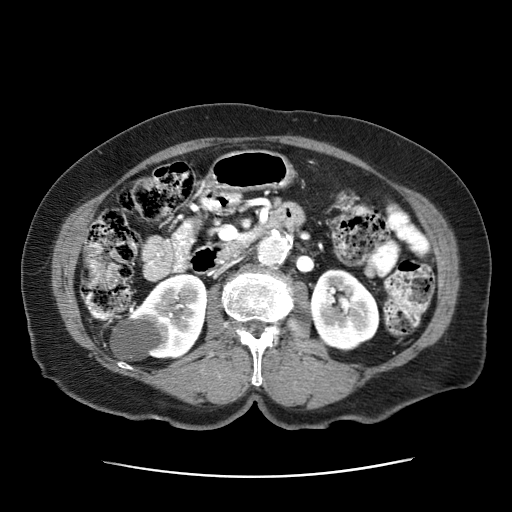
Contrast-enhanced abdominal CT (liver protocol), one axial slice. Position 5 of 63 along the scan axis. Reconstruction kernel STANDARD. 120 kVp. Intravenous contrast given. Soft-tissue window (W 400 / L 40 HU). 2.5 mm slice thickness. 512 × 512 image matrix, field of view 360 × 360 mm. Female patient, age 79 years. From the clinical record (not read from this slice): diagnosis: hepatocellular carcinoma (patient treated with transarterial chemoembolisation; whether this scan precedes or follows treatment is not stated here); TNM stage (as recorded): Stage-II.
Annotated regions visible in this slice (semi-automatic segmentation, software-assisted and operator-edited):
- abdominal aorta: bounding box [x1, y1, x2, y2] px = [258, 232, 293, 266]